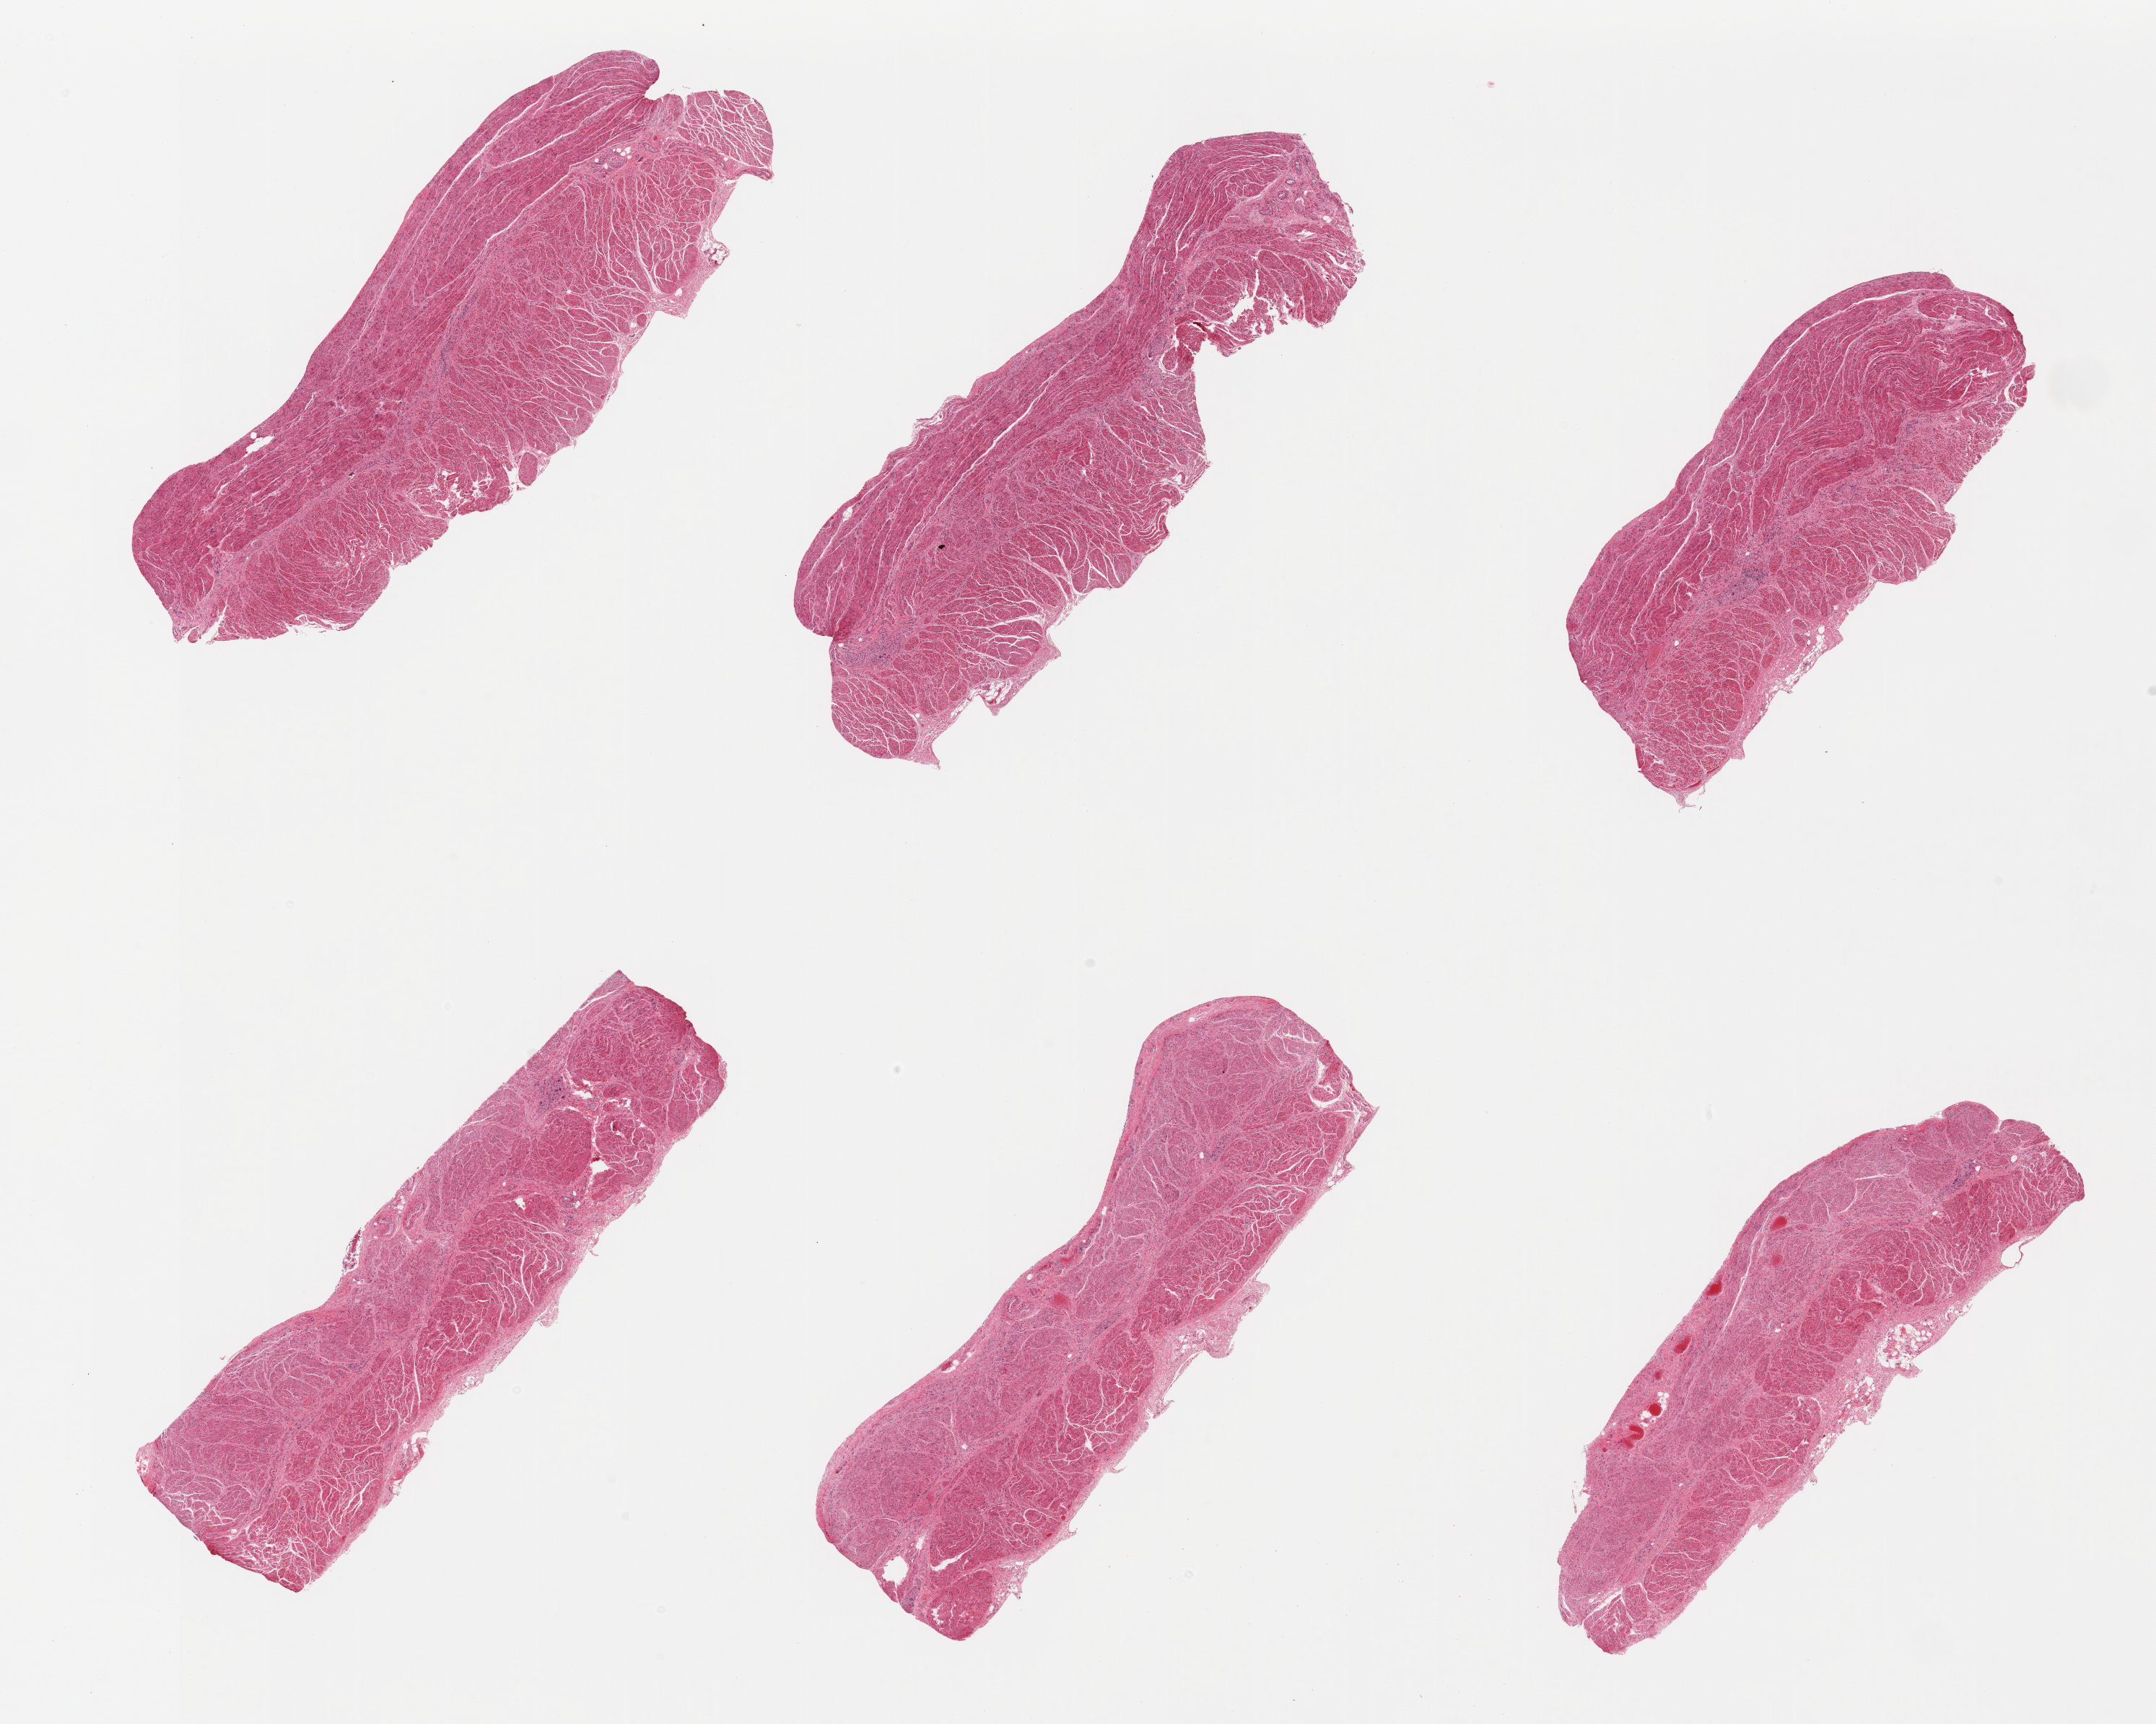
Whole-slide image, hematoxylin and eosin (H&E) stain, whole scanned area (about 23.6 x 18.9 mm) shown as a low-resolution overview, PAXgene-fixed paraffin-embedded (PFPE) section, target tissue: esophageal muscle, donor tissue sample. Donor sex: male.
Pathologist's review note for this sample: 6 pieces; well trimmed; inflammation around ganglion cells.